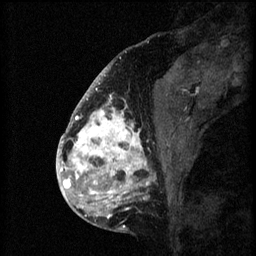
Breast MRI (dynamic contrast-enhanced), one sagittal slice. Position 27 of 60 along the scan axis. 3 images stored at this slice position (order not interpretable as contrast timing). 1.5 T. TE 4.2 ms, TR 8.2 ms. 2 mm slice thickness. 256 × 256 image matrix, field of view 180 × 180 mm. Female patient, age 41 years.
Annotated regions visible in this slice (semi-automatic segmentation, software-assisted and operator-edited):
- analysis volume of interest (the breast-tissue region the enhancement analysis was run in; not a lesion): bounding box [x1, y1, x2, y2] px = [72, 108, 176, 205]
- tumour enhancement mask (voxels above the 70 % enhancement threshold inside the analysis volume of interest): [72, 108, 151, 205]